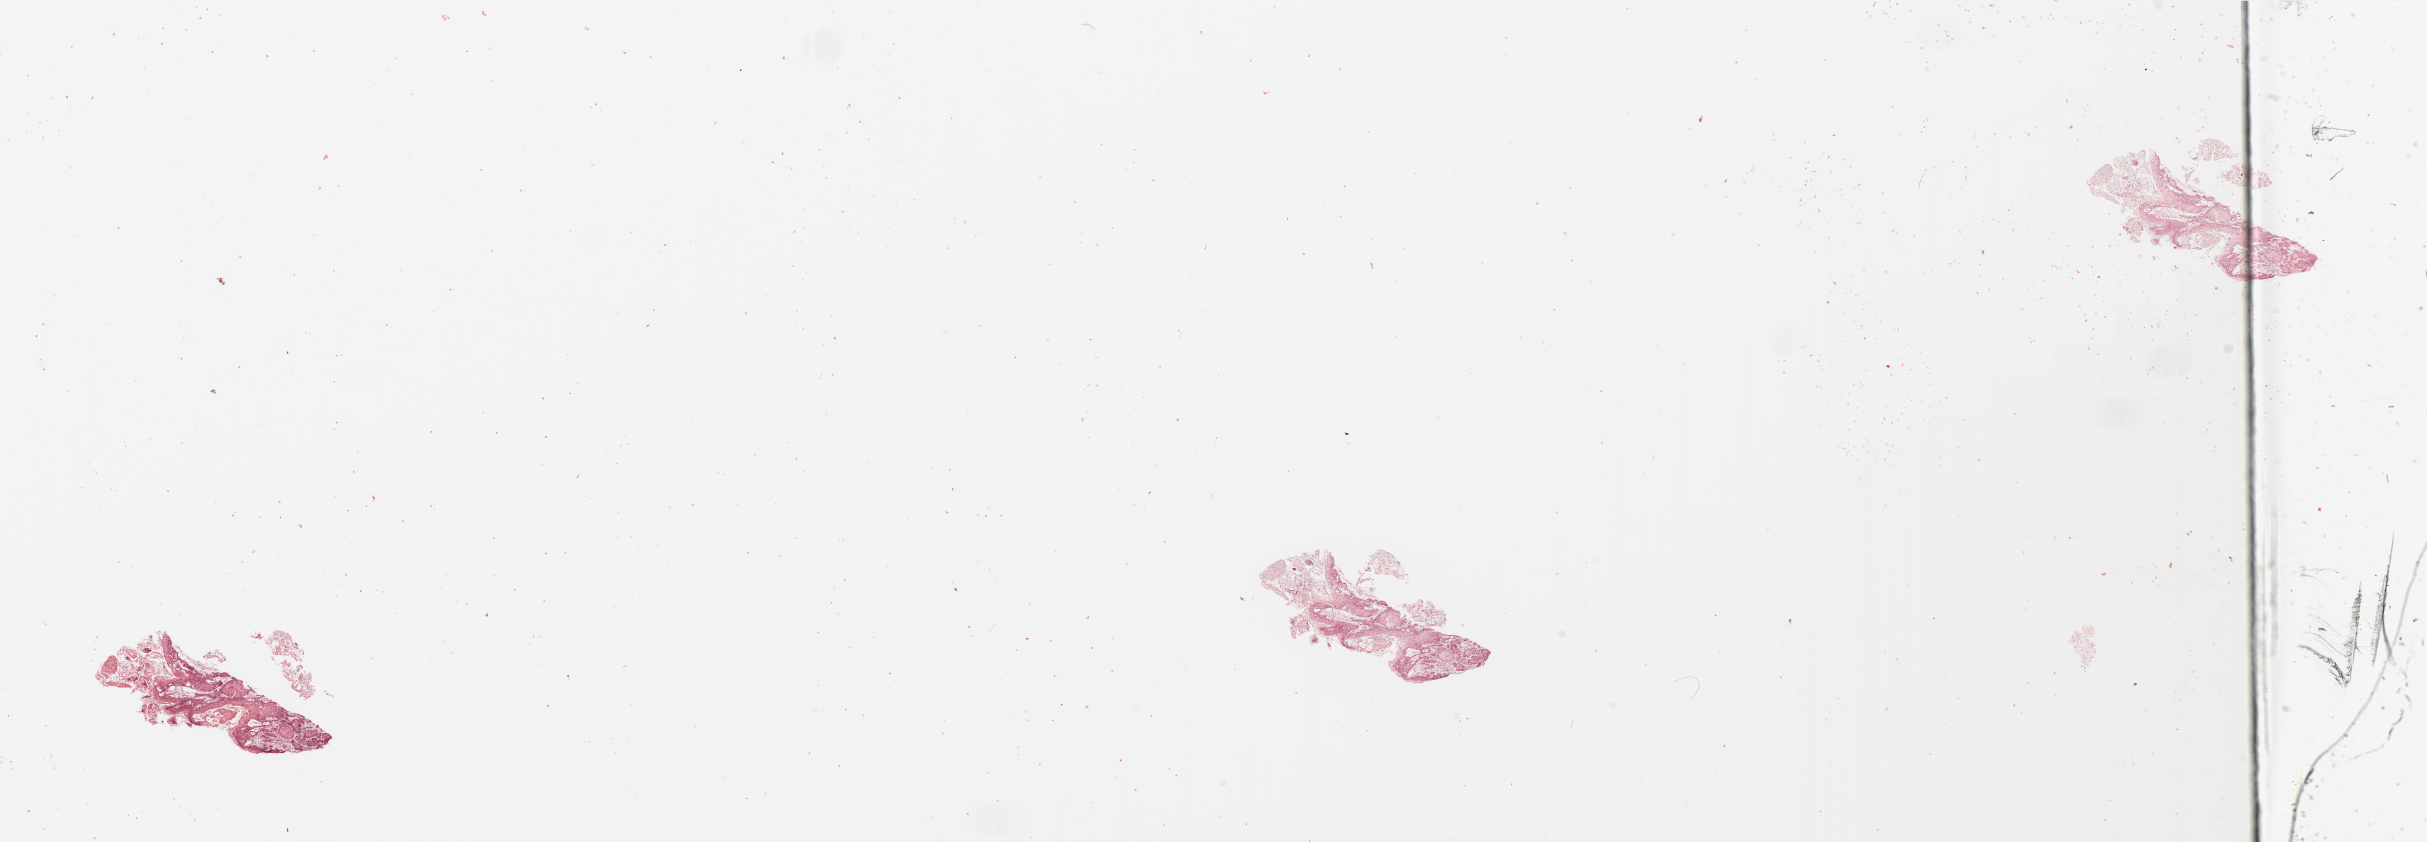
H&E whole-slide image — a low-resolution overview of the entire scanned area, about 38.4 x 13.3 mm, tumour tissue sample, sampled site: tongue. Patient: male, age 64 years. Histologic grade: G2 (moderately differentiated). Composition of this section per pathologist review: tumour nuclei 80%, necrosis 2%.
Histologic diagnosis: Squamous cell carcinoma, NOS (tongue, NOS). AJCC pathologic stage: III.